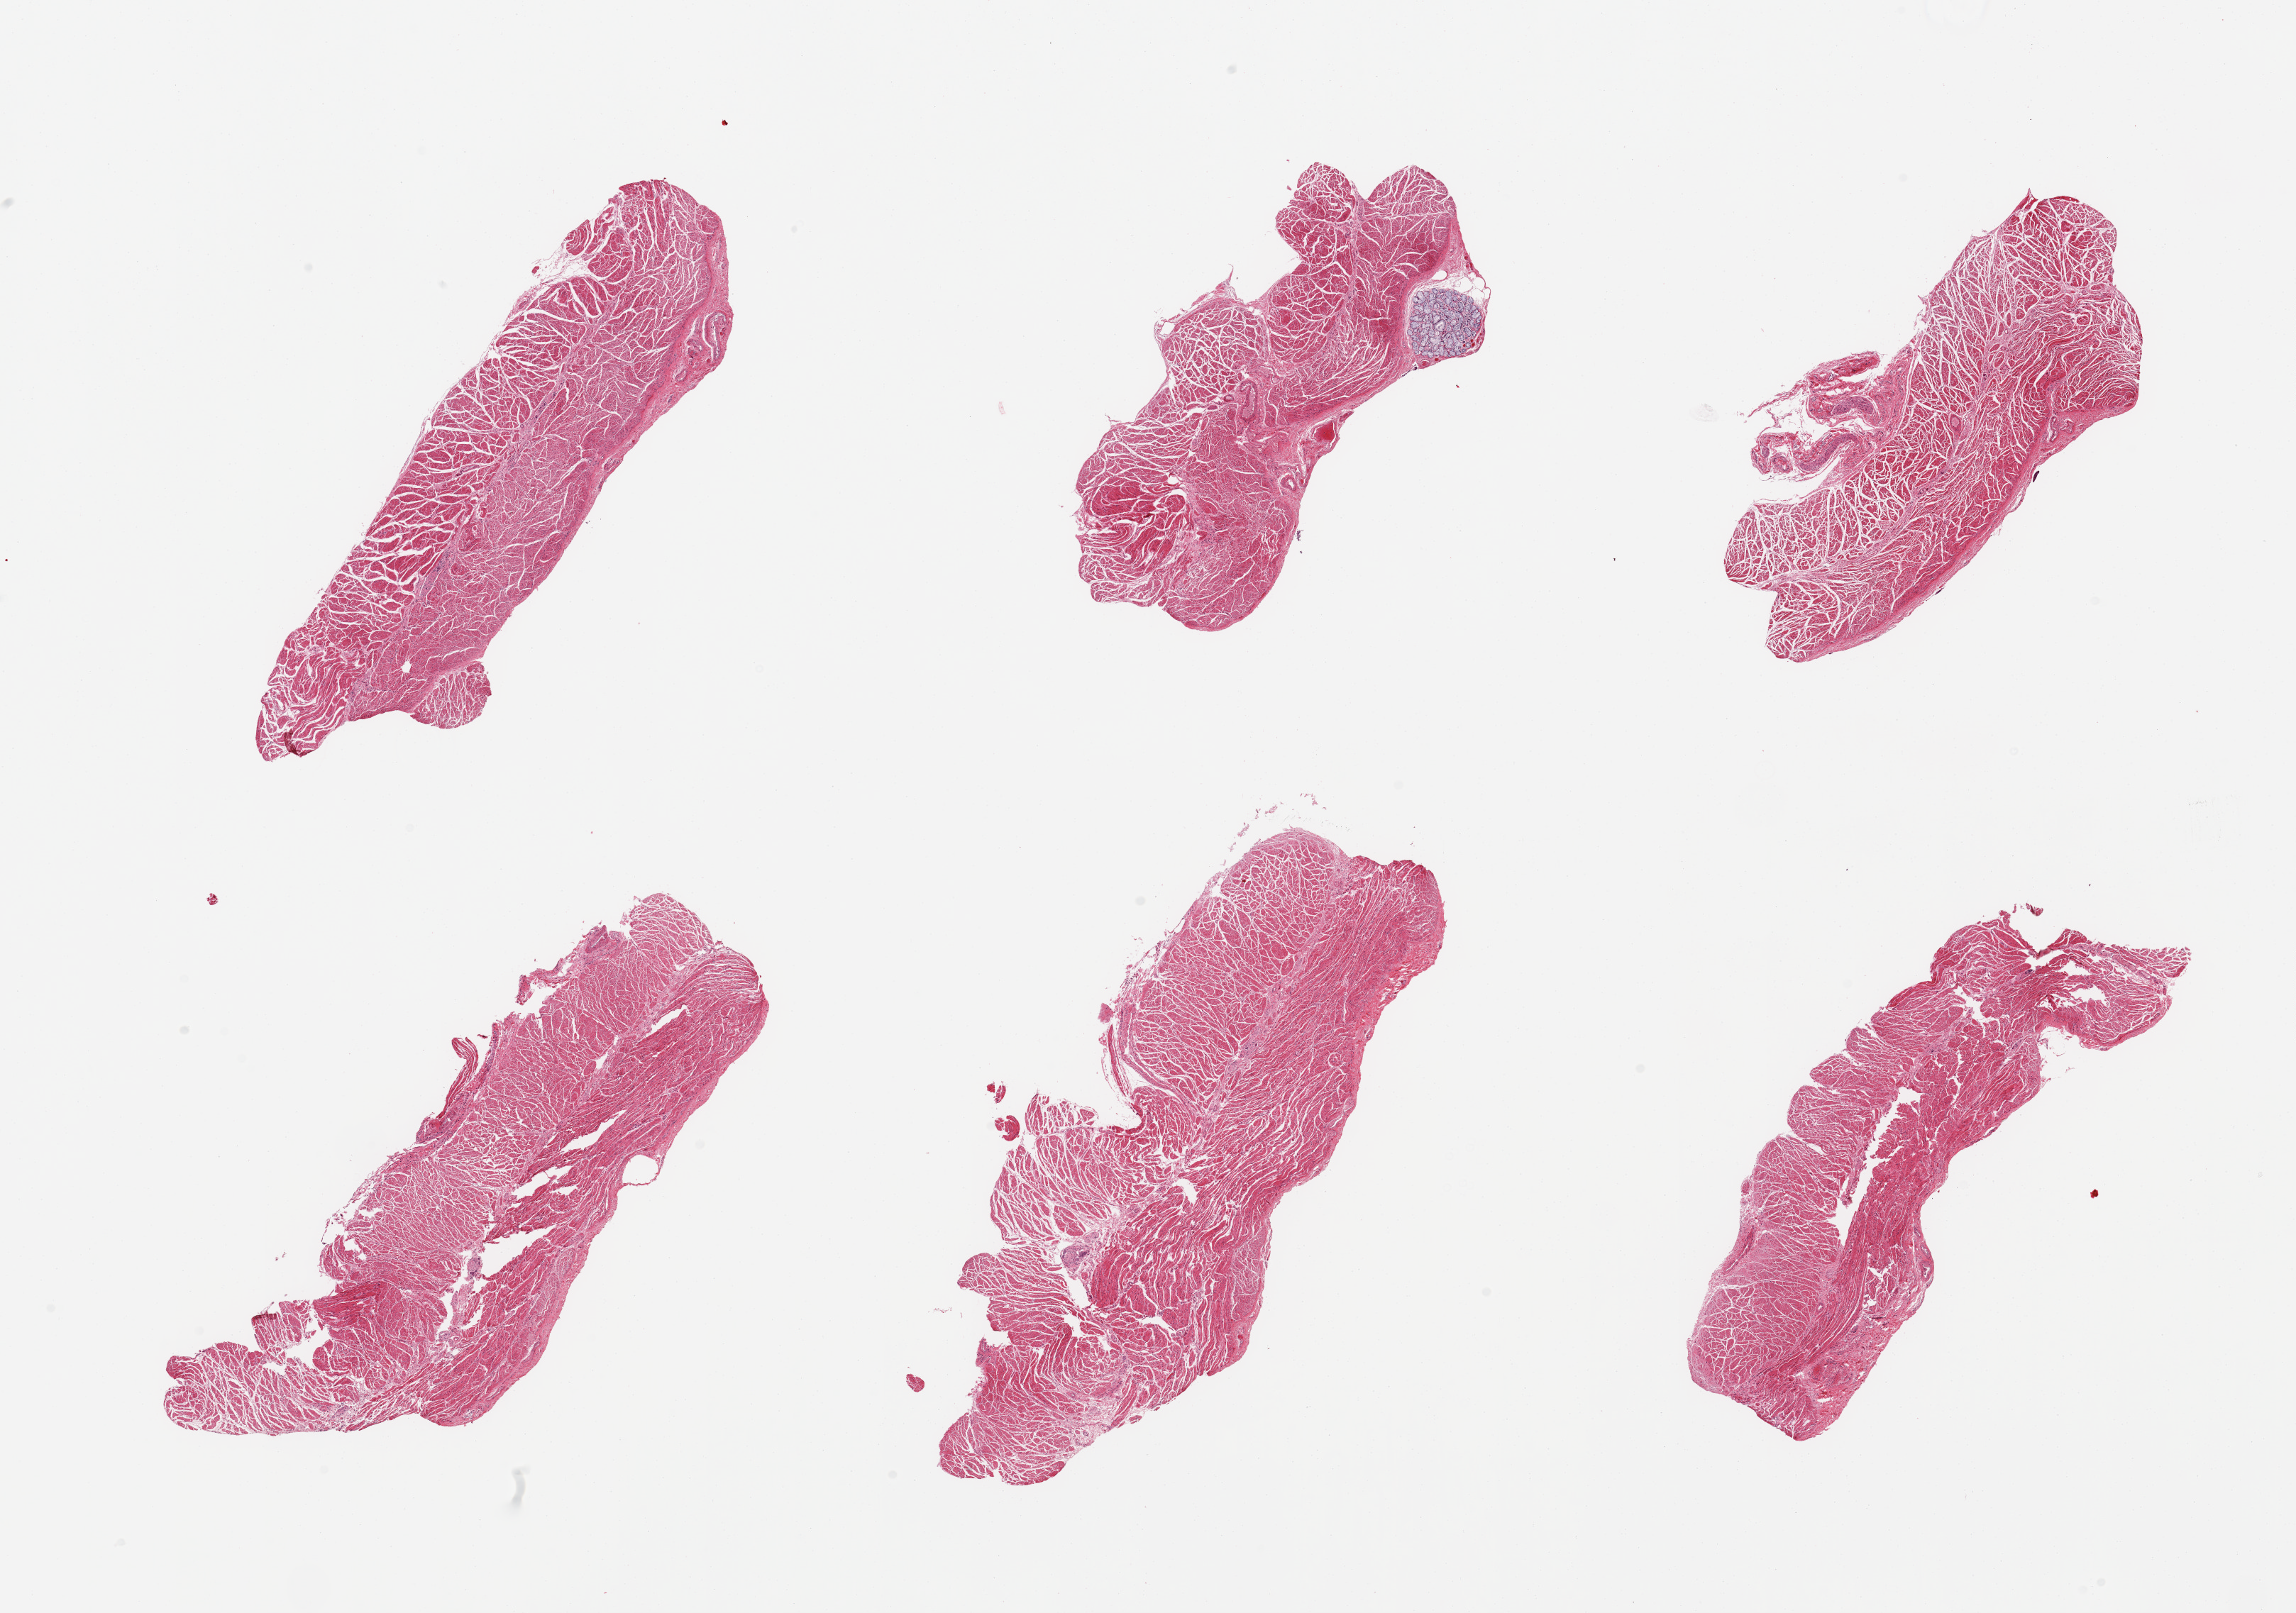
Whole-slide image, H&E stain — low-resolution overview of the scanned area, about 25.6 x 18.0 mm (from a 20x scan), PAXgene-fixed, paraffin-embedded tissue, section of esophageal muscle (target tissue), tissue donor sample. Donor: male.
• pathologist's review note for this sample: 6 pieces; muscularis with rare cluster of submucosal glands